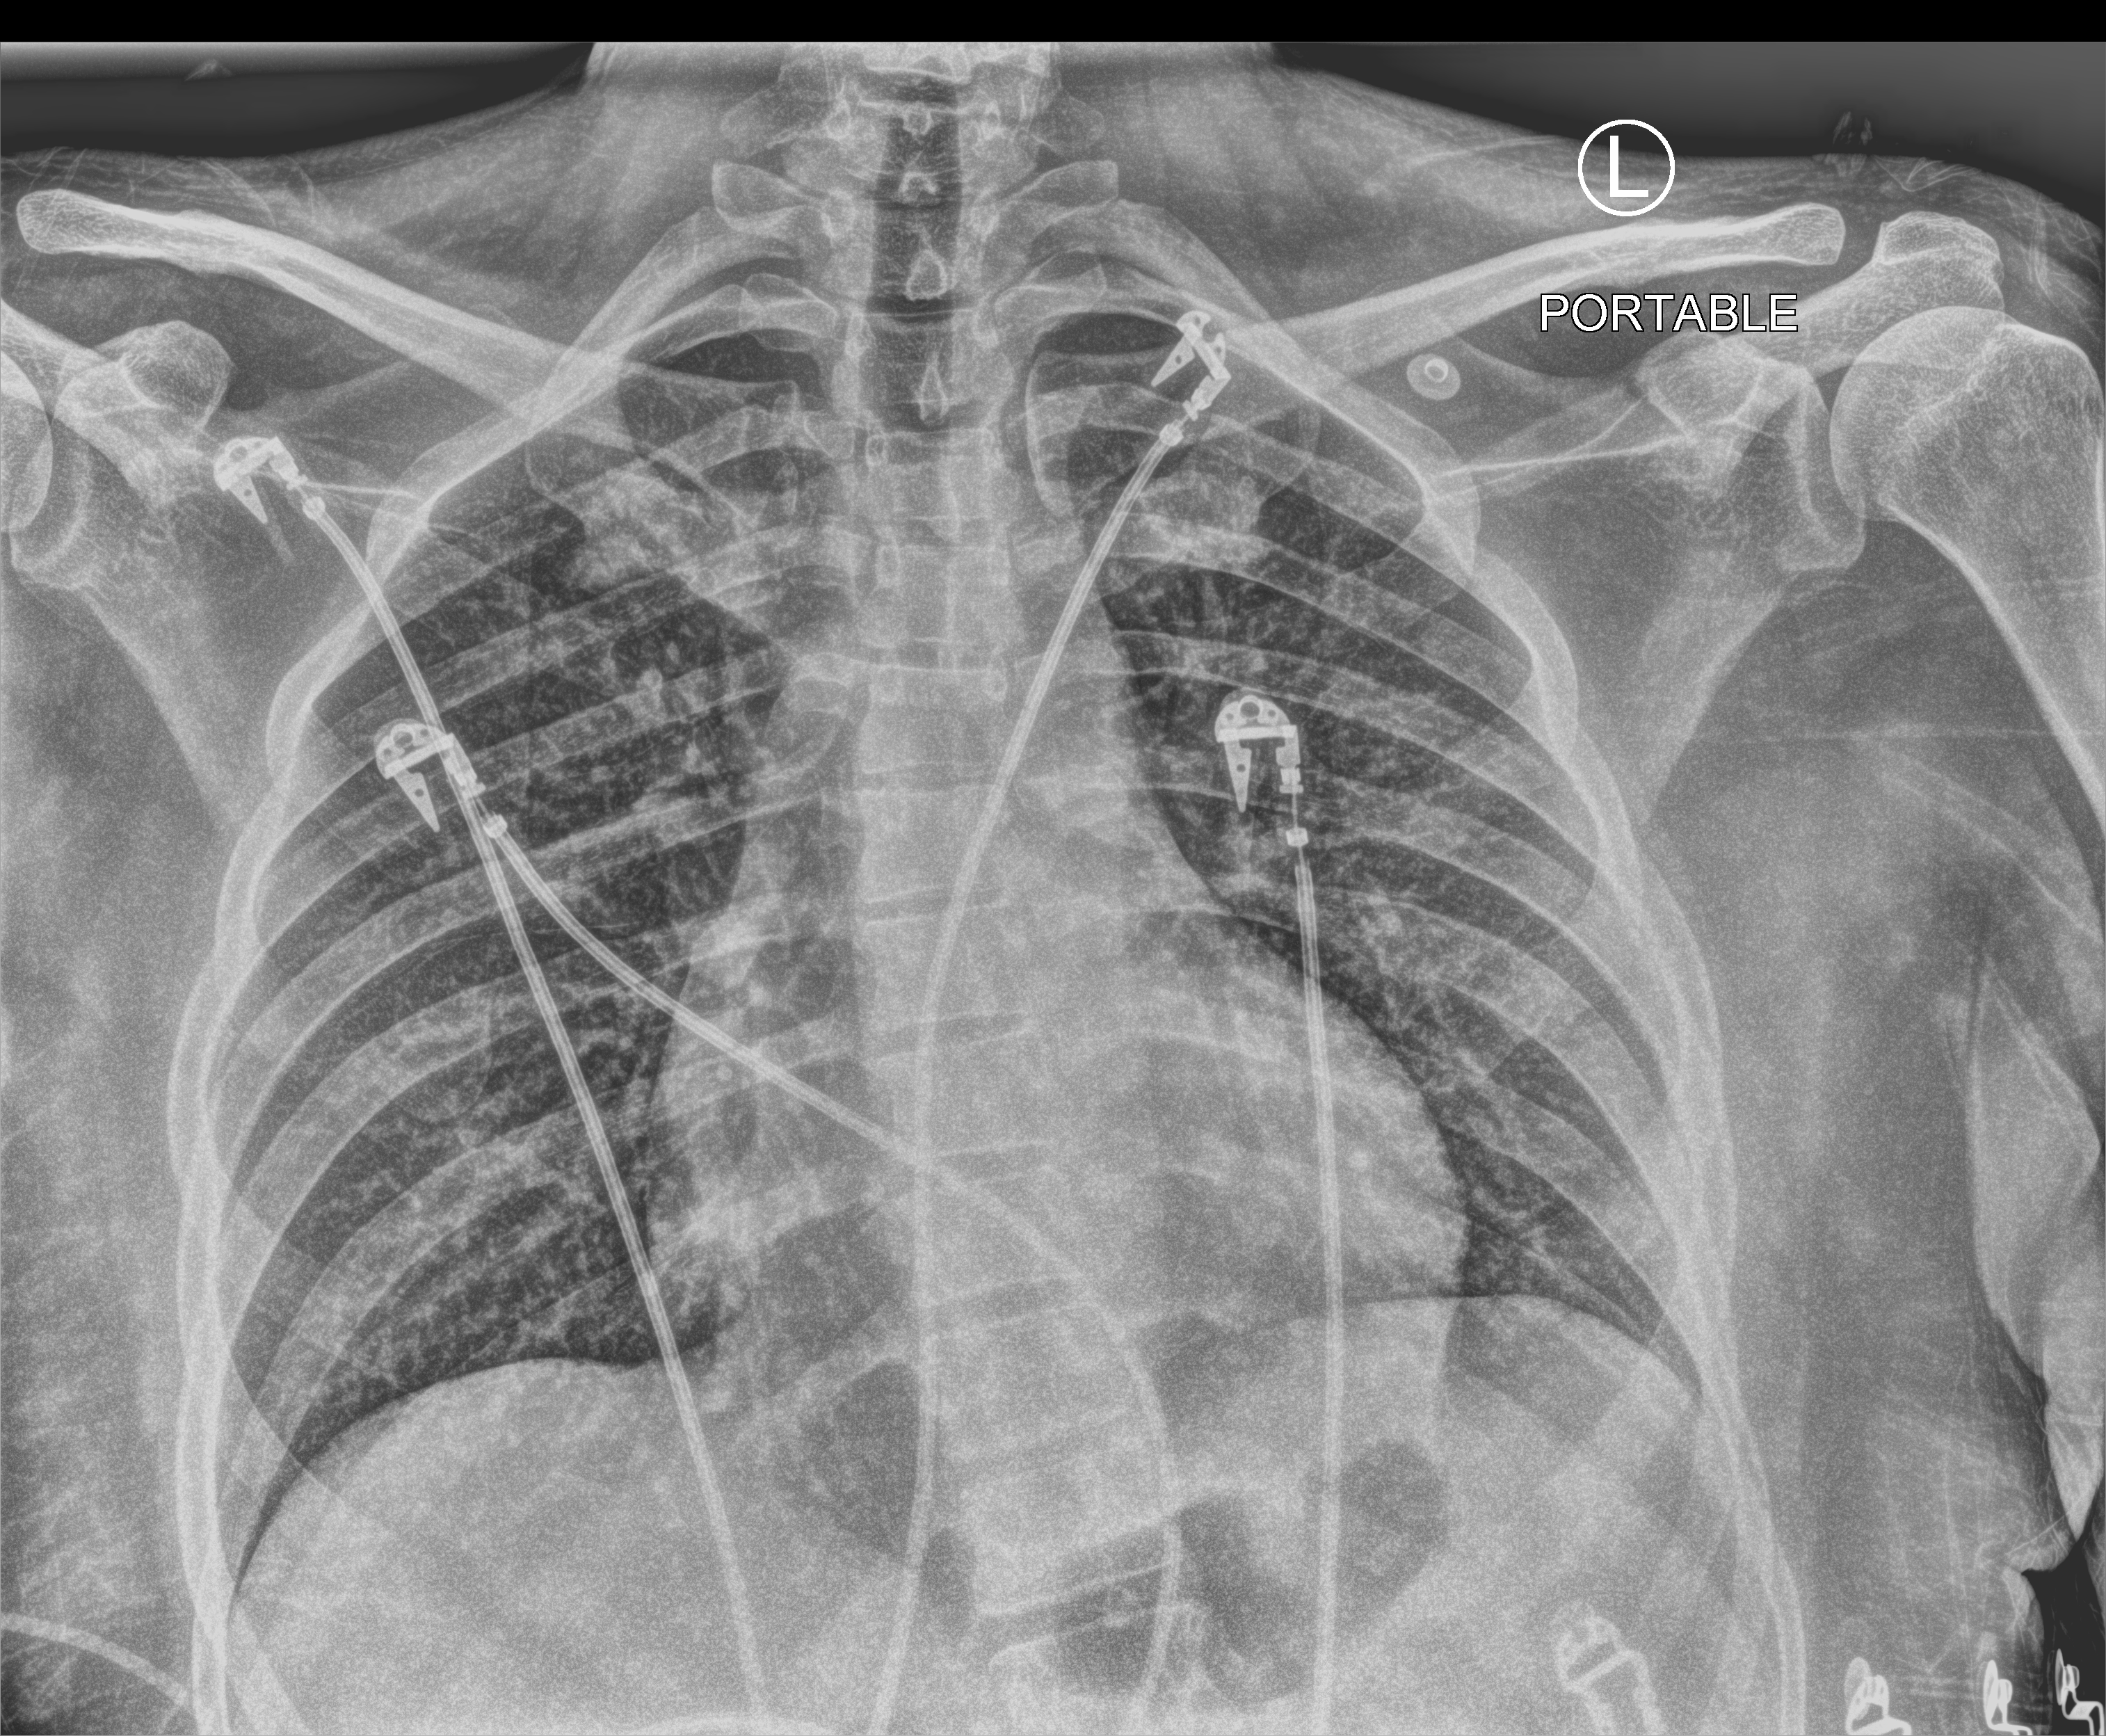
Bedside chest radiograph (computed radiography); anteroposterior (AP) projection. Patient hospitalised with COVID-19; male, aged 18–59 years.
From the hospital-stay record, not from the radiograph (when in the stay this image was taken is not recorded): length of hospital stay: 2 days.